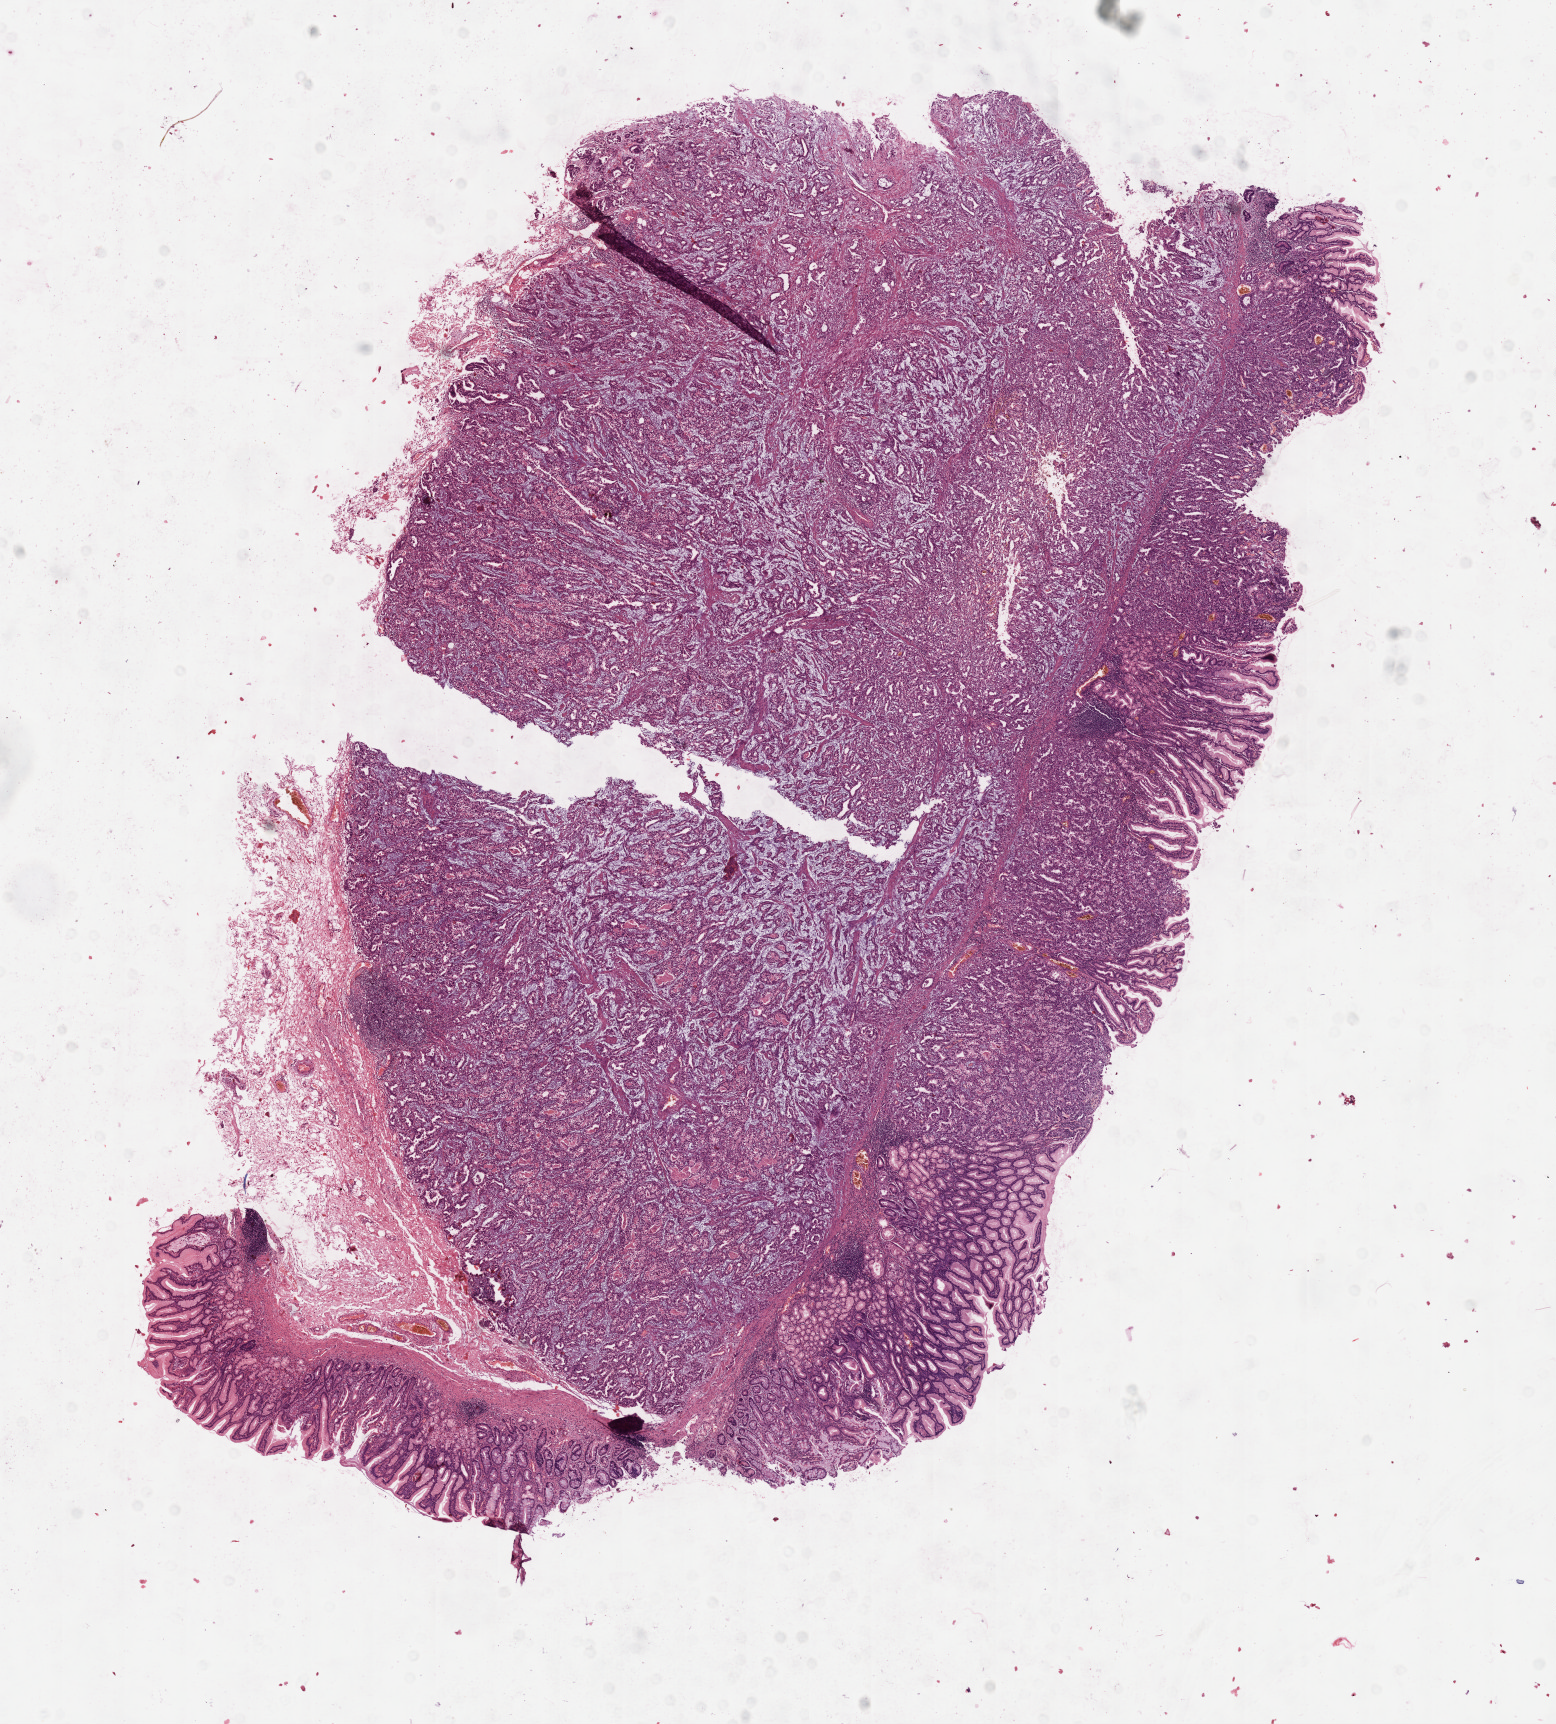
Whole-slide histology image, H&E, a low-resolution overview of the entire scanned area, about 12.6 x 13.9 mm (acquisition: 40x scan), formalin-fixed paraffin-embedded (FFPE) diagnostic section, sample: primary tumour, stomach. Male patient; age at initial diagnosis 45 years. Histologic grade: G2 (moderately differentiated).
* AJCC pathologic stage: IIIA (7th edition)
* diagnosis: Mucinous adenocarcinoma
* TNM: T3 N2 M0
* lymph nodes positive (case pathology): 3 of 5 examined